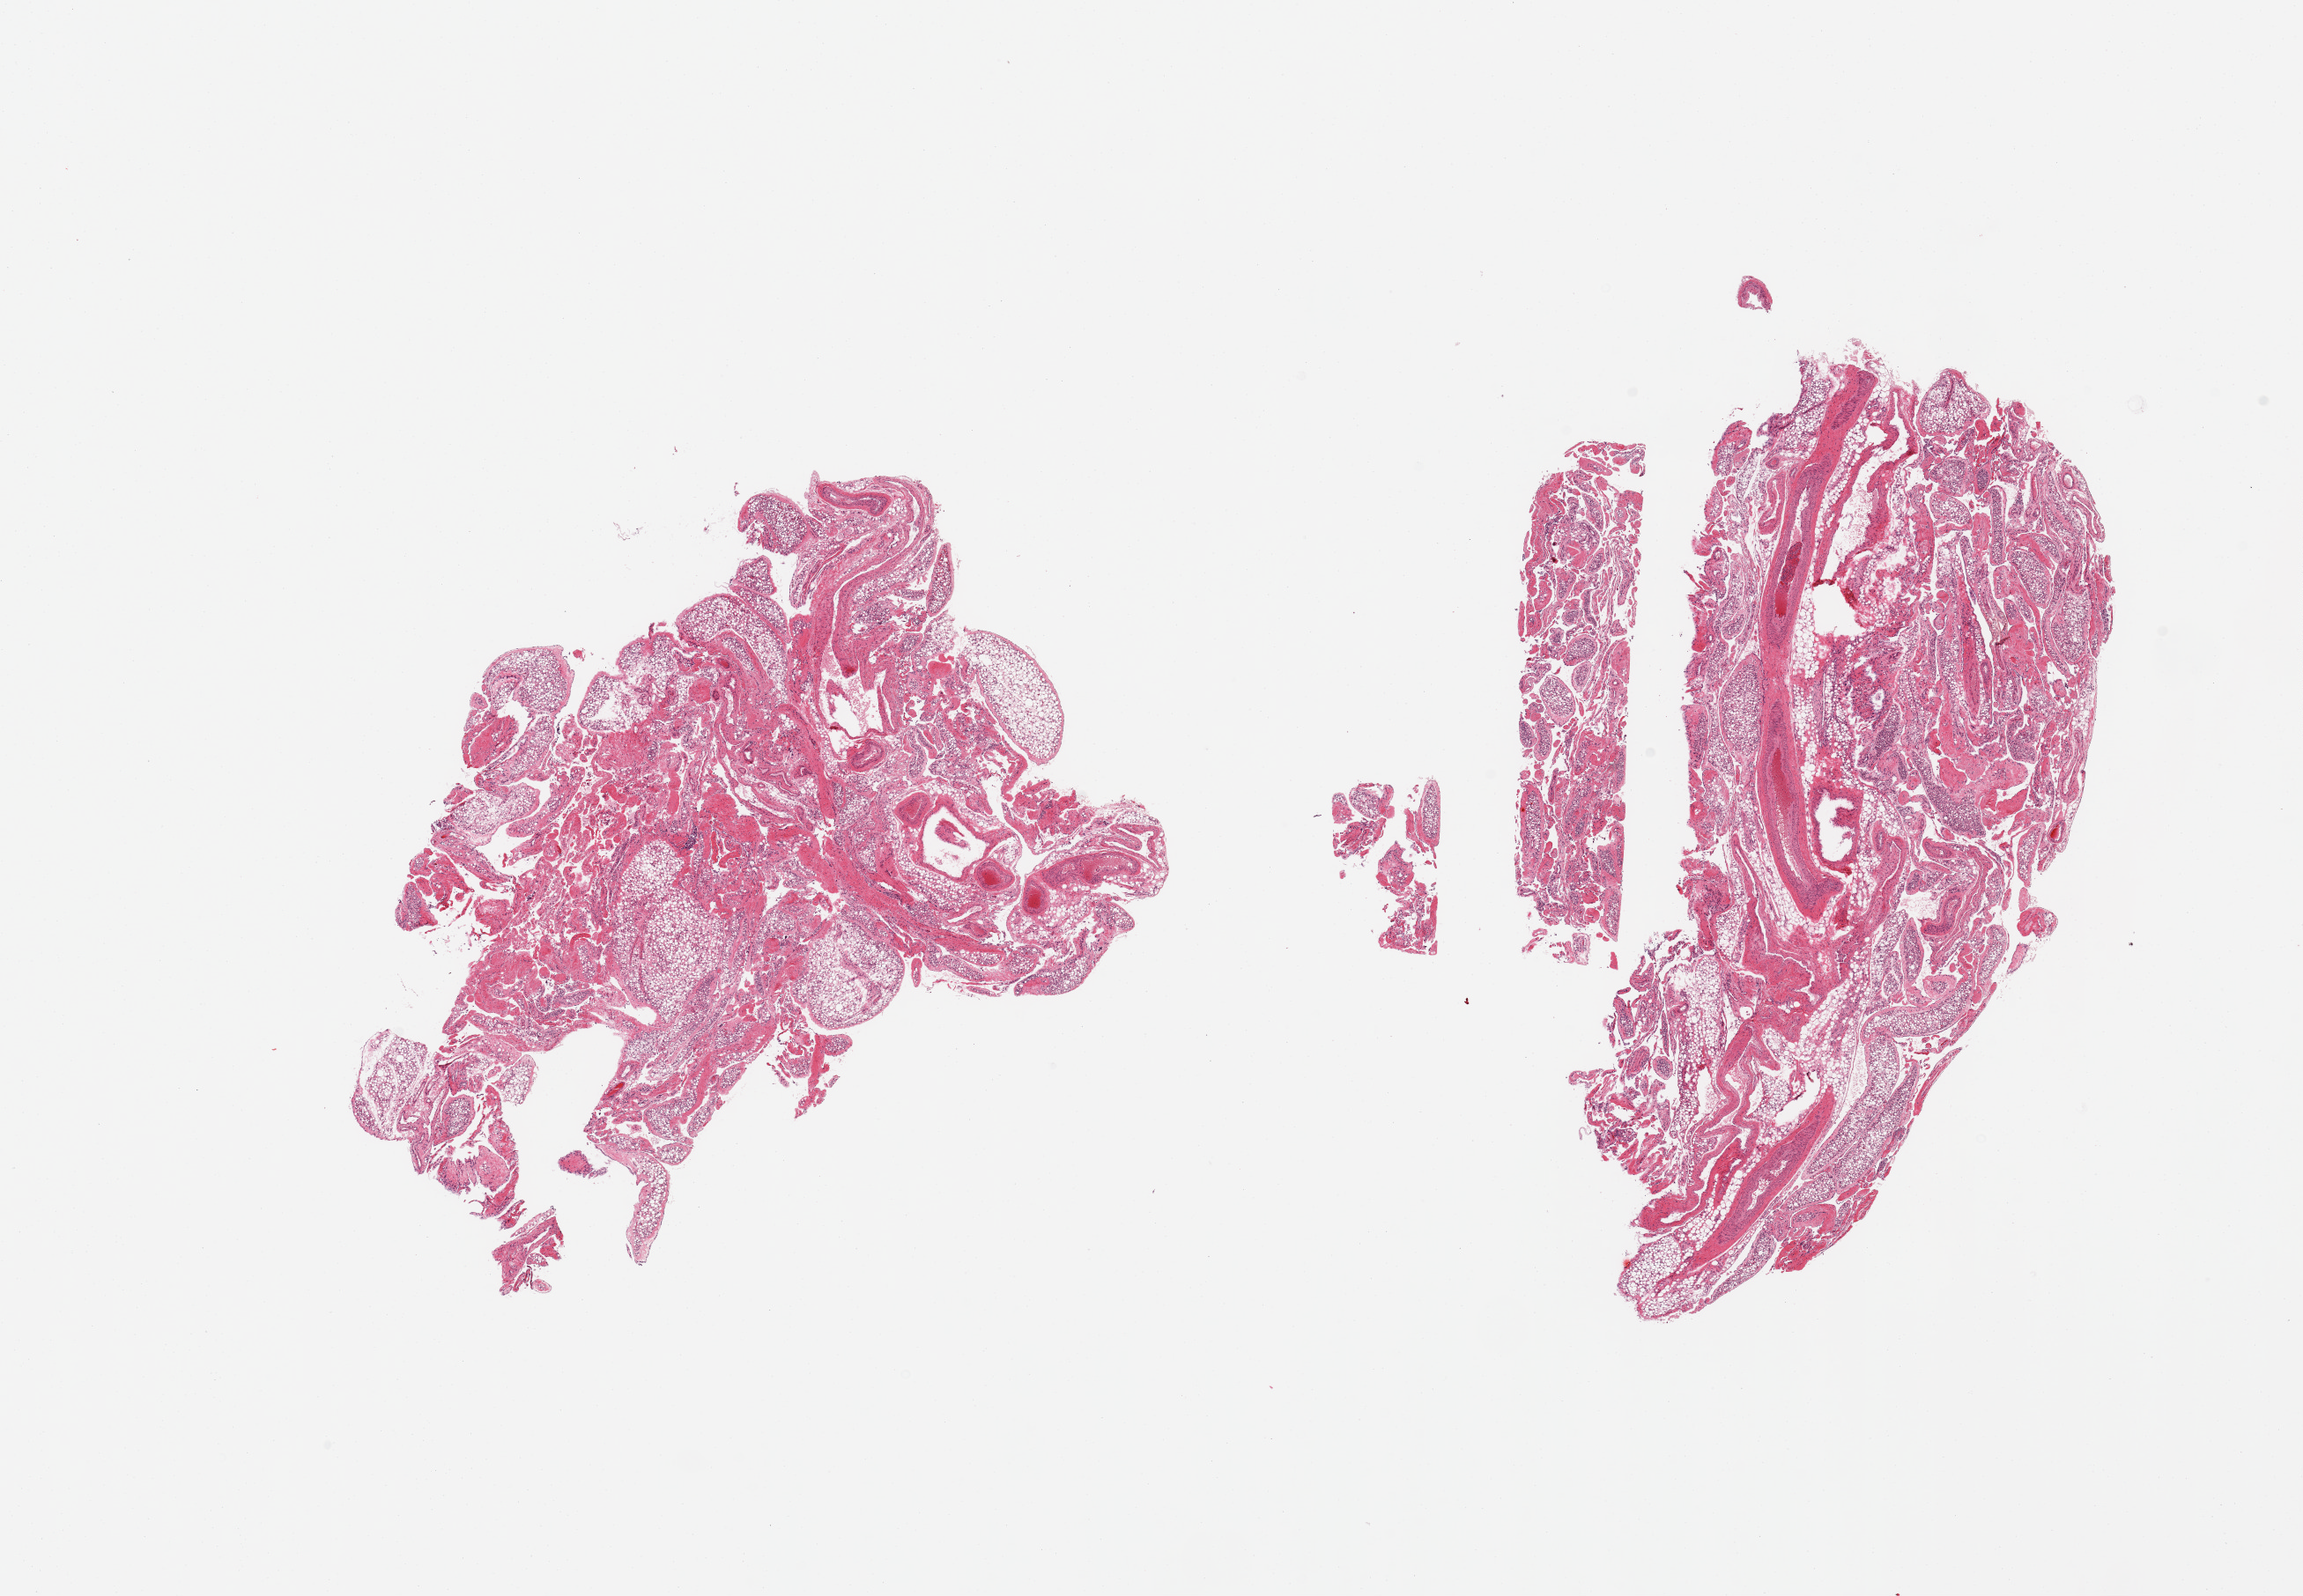
Whole-slide image, H&E stain, whole scanned area (about 20.7 x 14.3 mm) shown as a low-resolution overview, PAXgene-fixed paraffin-embedded (PFPE) section, sampled site (target tissue): omentum, donor tissue sample. Donor sex: male.
* reviewer comment on this tissue sample: 2 pieces; depleted fat comprises 50%, remainder is fibrovascular